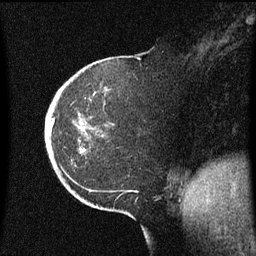
Breast MRI (dynamic contrast-enhanced), one sagittal slice. Slice 17 of 60 in the series (ordered by position). Dynamic contrast-enhanced series, image 2 of 3 at this slice position (ordered by acquisition). 1.5 T. TE 4.2 ms, TR 8.4 ms. 256 × 256 image matrix, field of view 200 × 200 mm. Patient: female, 38 years. Case-level facts recorded for this patient, not image findings: setting: breast cancer imaged before/during neoadjuvant chemotherapy; receptor status: HER2-positive.
Outlined on this slice (semi-automatic segmentation, software-assisted and operator-edited):
- analysis volume of interest (the breast-tissue region the enhancement analysis was run in; not a lesion): bounding box [x1, y1, x2, y2] px = [45, 54, 143, 185]
- tumour enhancement mask (voxels above the 70 % enhancement threshold inside the analysis volume of interest): [53, 118, 55, 123]